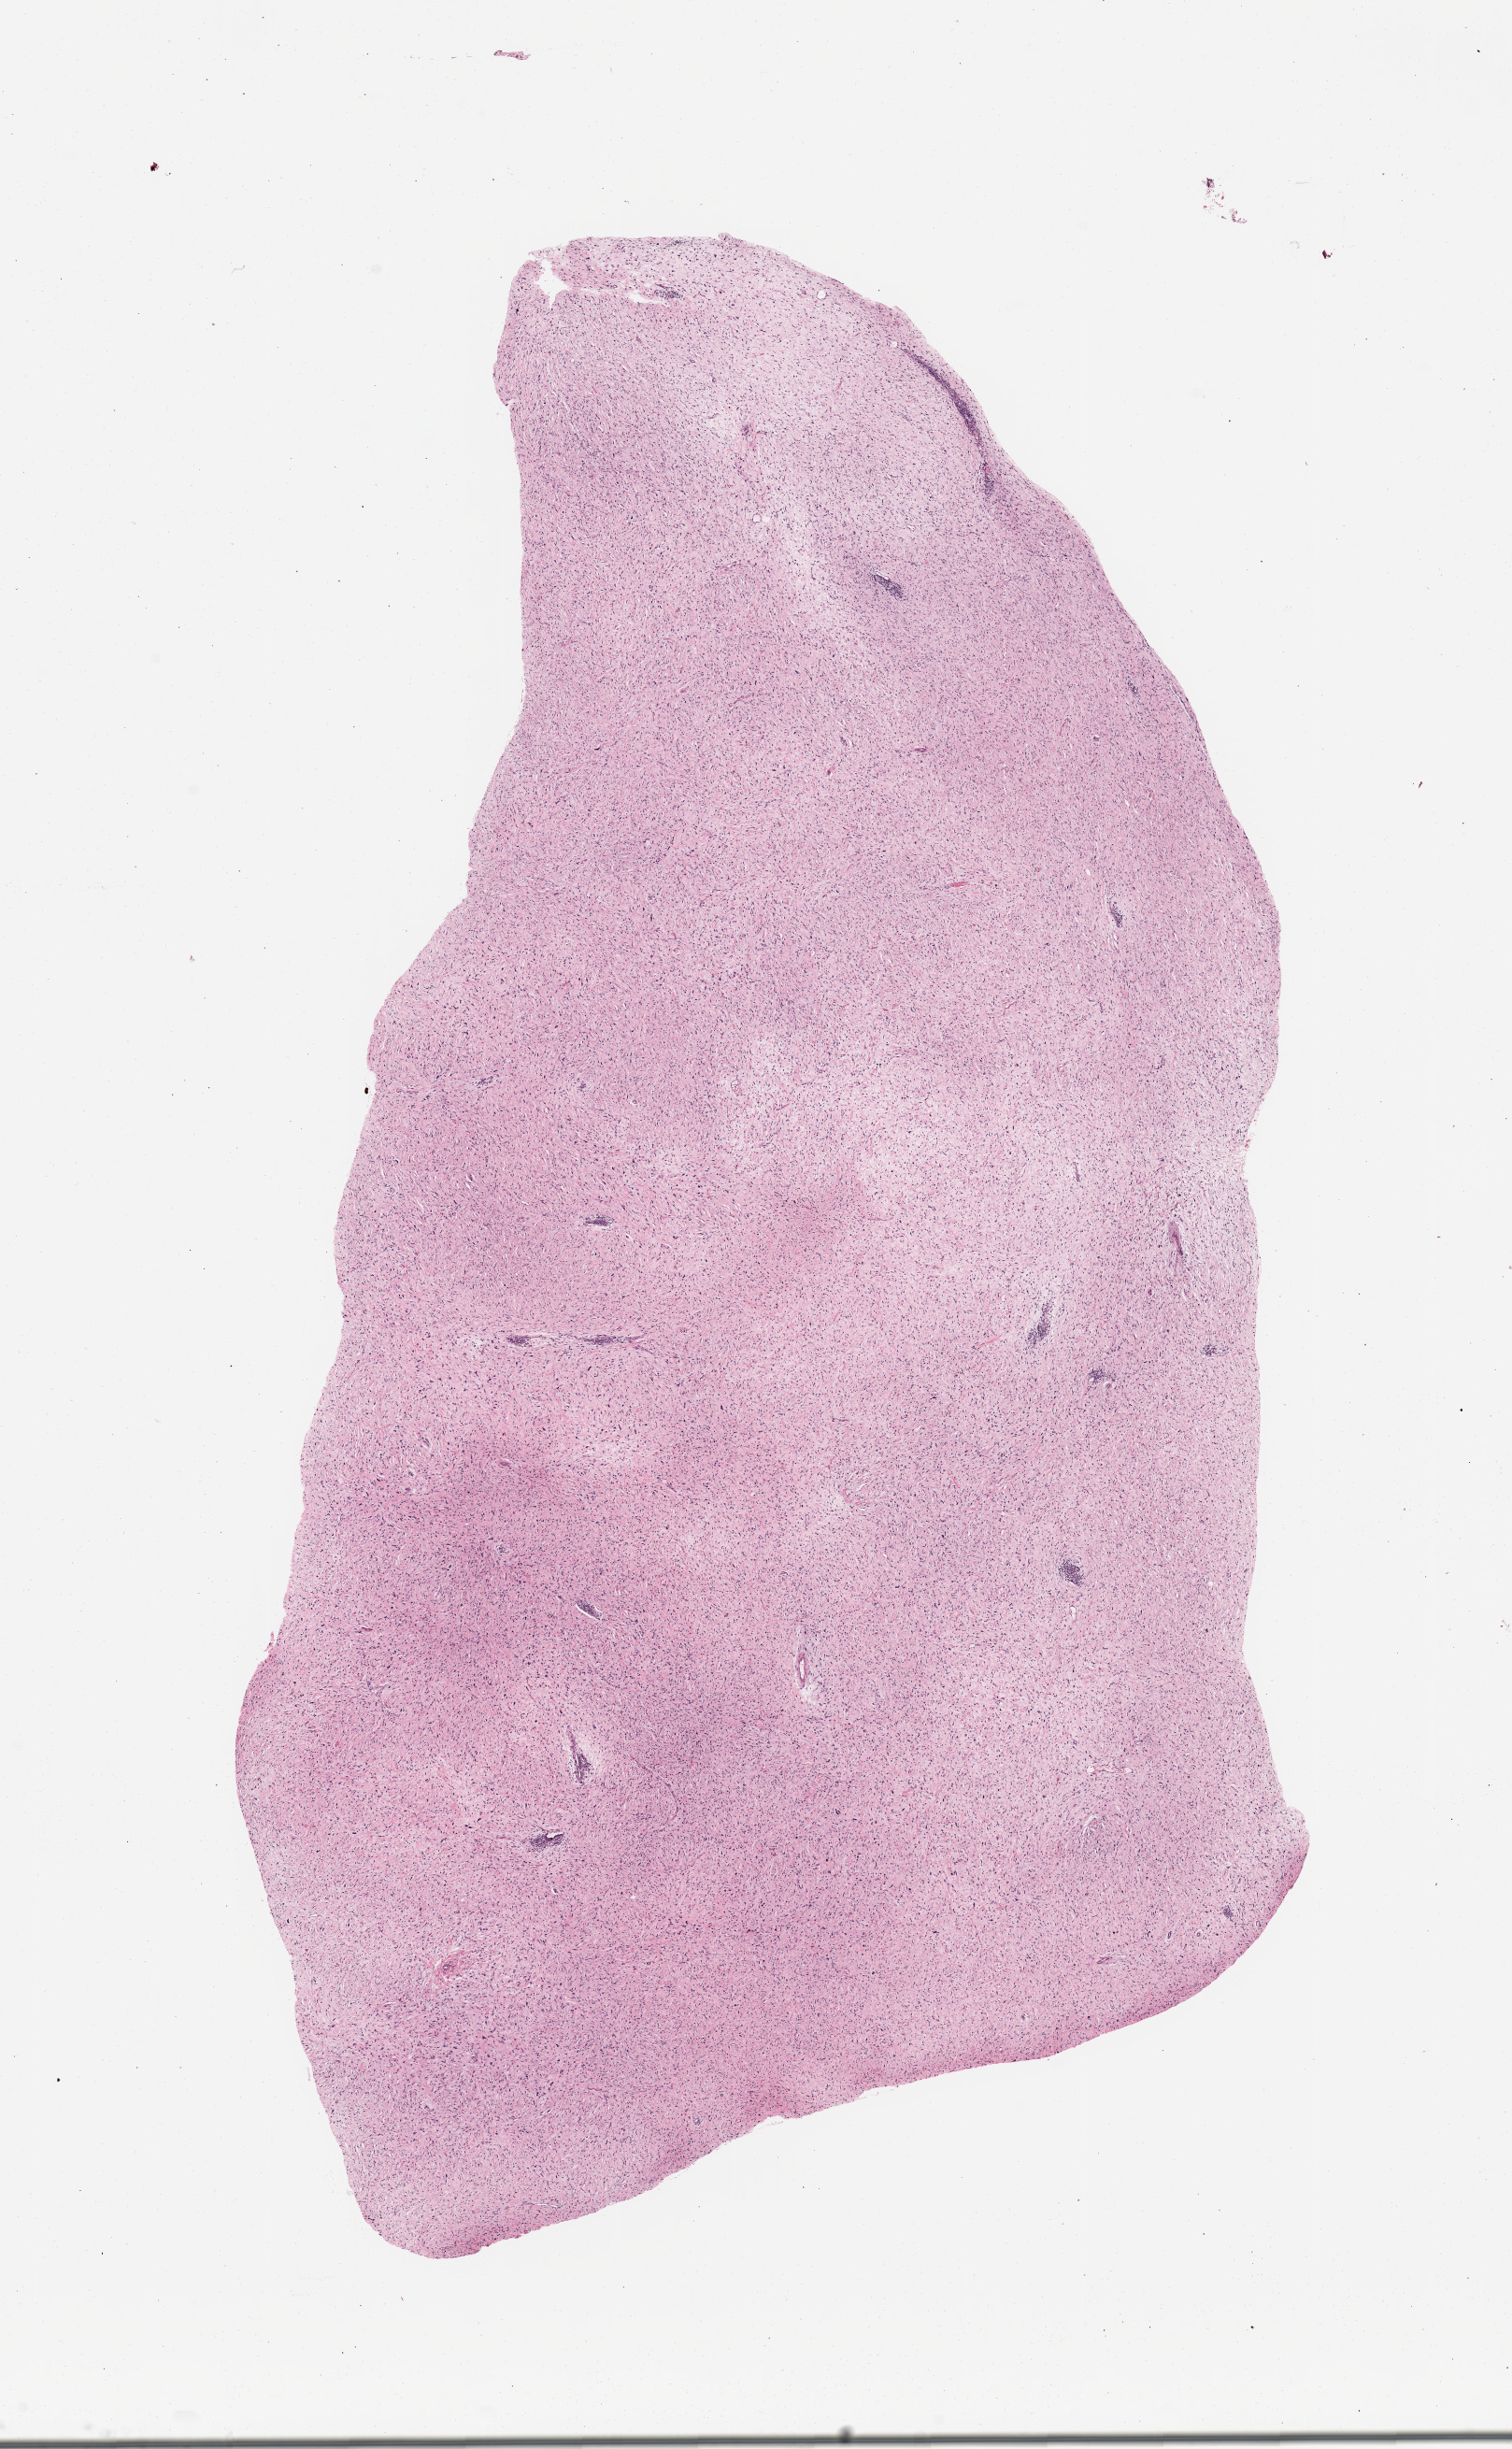
Digitized H&E-stained tissue section (whole slide), whole scanned area (about 12.8 x 20.7 mm, slide scanned at 20x) shown as a low-resolution overview. Tumour tissue sample. Patient: female, age 54 years.
Patient diagnosis (cohort enrolment): sarcoma (site not recorded at cohort level). Primary tumour site (as recorded): retroperitoneum.